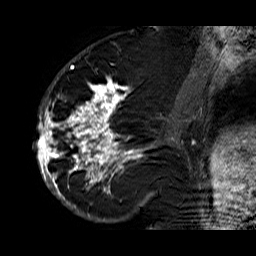
Breast MRI (dynamic contrast-enhanced), one sagittal slice. Slice 27 of 60 in the series (ordered by position). Dynamic contrast-enhanced series, time point 2 of 6 at this slice position (early post-contrast). 1.5 T. TE 6.3 ms, TR 32.9 ms. 4 mm slice thickness. 256 × 256 image matrix. Female patient. From the clinical record (not read from this slice): setting: breast cancer imaged before/during neoadjuvant chemotherapy; receptor status: HR-positive, HER2-negative.
Structures marked on this image (semi-automatically segmented with operator editing):
- analysis volume of interest (the breast-tissue region the enhancement analysis was run in; not a lesion): bounding box (x1, y1, x2, y2) in pixels: (33, 74, 176, 210)
- tumour enhancement mask (voxels above the 100 % enhancement threshold inside the analysis volume of interest): (35, 79, 176, 210)